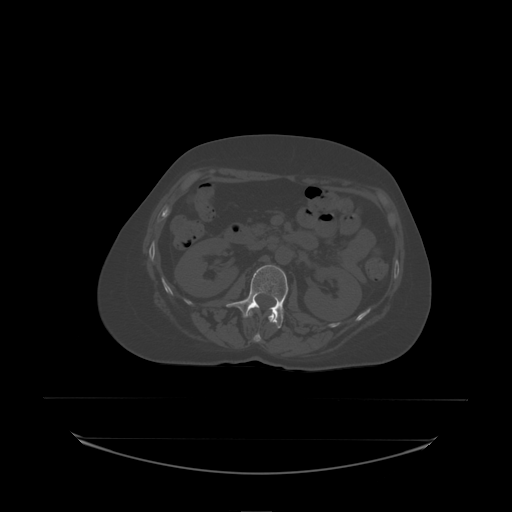
CT including the spine, one axial slice; slice 75 of 242 in the series (ordered by position); bone window (W 1800 / L 400 HU); 2.5 mm slice thickness; 512 × 512 image matrix, field of view 500 × 500 mm. Patient: female, 53 years. From the clinical record (not read from this slice): primary cancer: lung; vertebrae with lytic lesions (as recorded): T7, L1.
Structures marked on this image (semi-automatic segmentation, software-assisted and operator-edited):
- L1 vertebra: bounding box (x1, y1, x2, y2) in pixels: (249, 308, 275, 338)
- L2 vertebra: (227, 265, 289, 329)